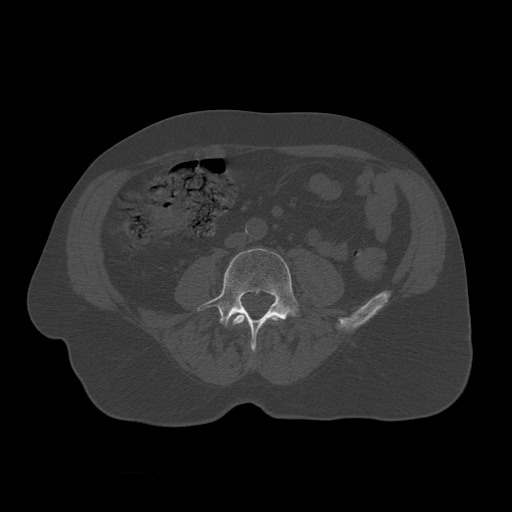
CT including the spine, one axial slice. Position 280 of 450 along the scan axis. Reconstruction kernel STANDARD. 120 kVp. Bone window (W 1800 / L 400 HU). 1.25 mm slice thickness. 512 × 512 image matrix. Patient age 75 years. Case-level facts recorded for this patient, not image findings: primary cancer: prostate.
Annotated regions visible in this slice (semi-automatically segmented with operator editing):
- L3 vertebra: bounding box (x1, y1, x2, y2) in pixels: (230, 313, 277, 353)
- L4 vertebra: (198, 248, 300, 351)
- L5 vertebra: (231, 319, 242, 327)